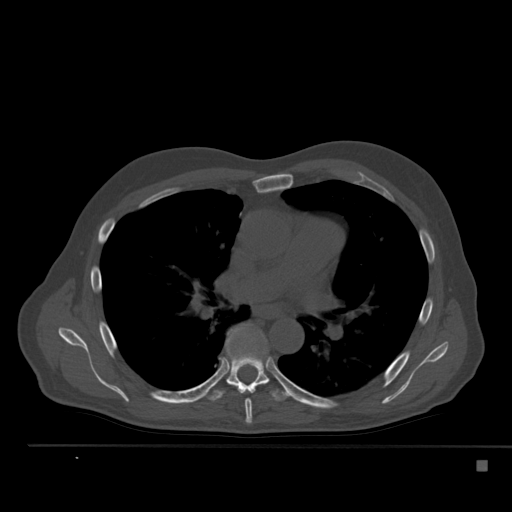
CT including the spine, one axial slice. Slice 336 of 517 in the series (ordered by position). Reconstruction kernel Br40s. 120 kVp. Bone window (W 1800 / L 400 HU). 512 × 512 image matrix, field of view 408 × 408 mm. Male patient, age 70 years. Case-level facts recorded for this patient, not image findings: primary cancer: renal; vertebrae with lytic lesions (as recorded): T4, T6, T10, T12, L3, L4, L5.
Structures marked on this image (semi-automatically segmented with operator editing):
- T6 vertebra: bounding box [x1, y1, x2, y2] px = [245, 399, 253, 424]
- T7 vertebra: [203, 325, 292, 401]